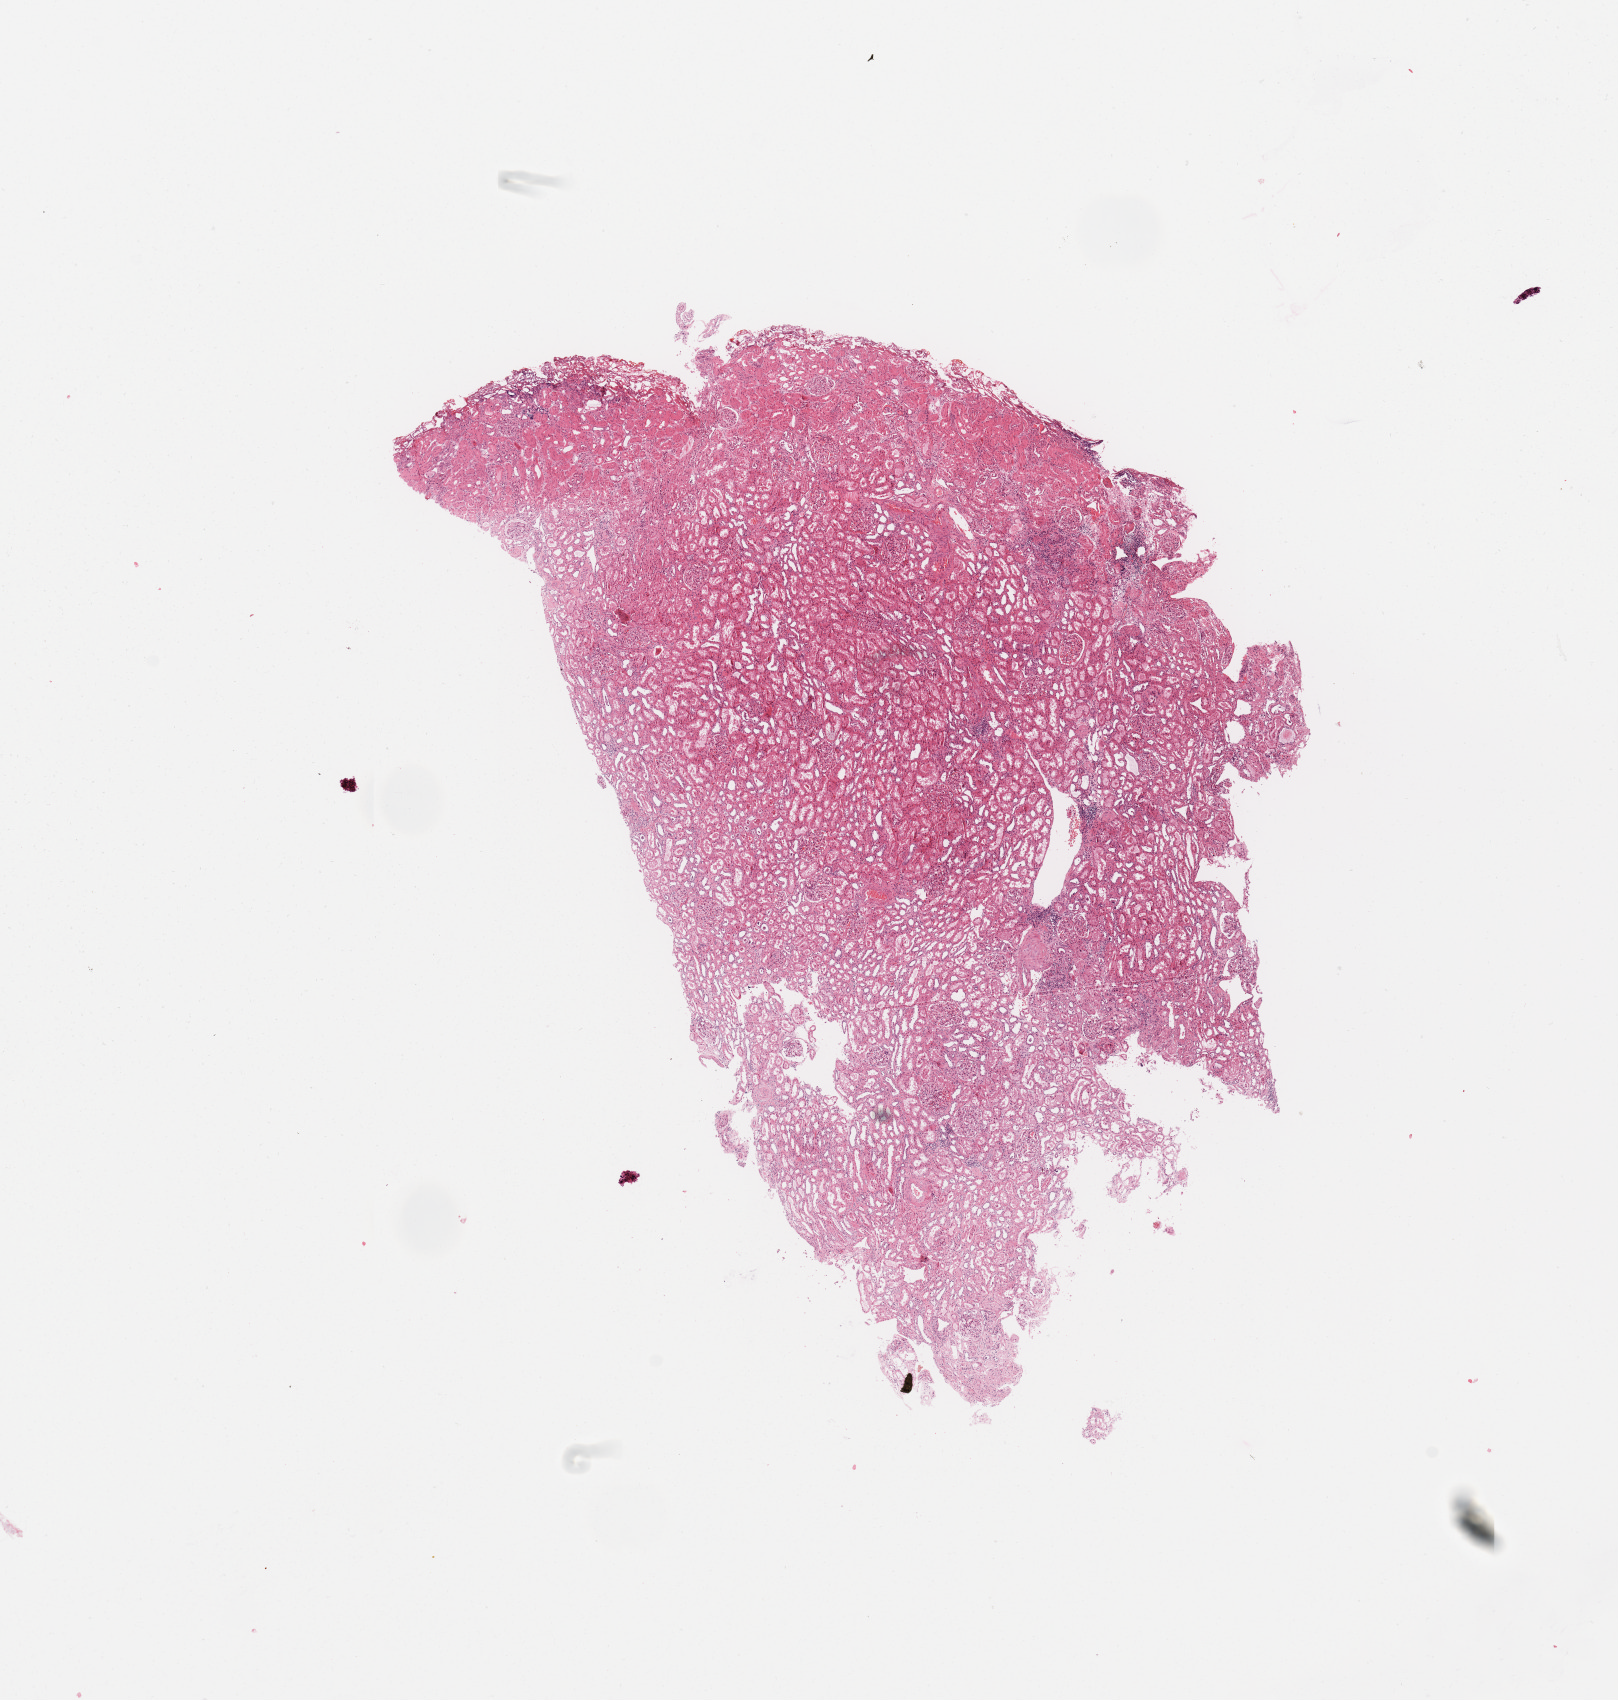
H&E whole-slide image — low-resolution overview of the scanned area, about 12.8 x 13.4 mm (from a 20x scan), normal (non-tumour) tissue sample, sampled site: kidney. 47-year-old male patient.
- this section: normal (non-tumour) tissue from the same patient
- patient diagnosis: Renal cell carcinoma, NOS